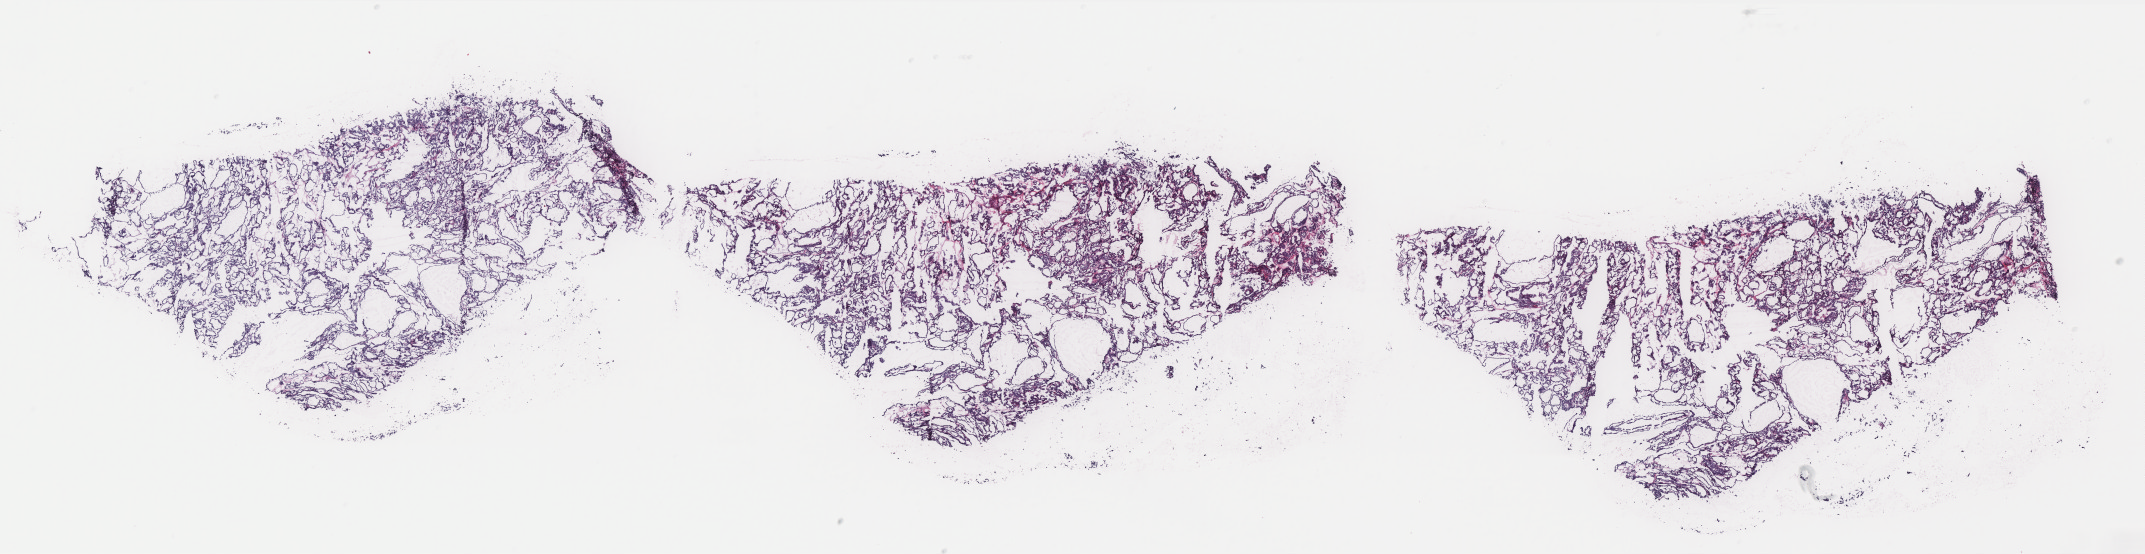
Whole-slide histology image, H&E, a low-resolution overview of the entire scanned area, about 34.4 x 8.9 mm (slide scanned at 40x). Frozen section from the top of the tissue portion. Sample: primary tumour, thyroid. Male patient; age at initial diagnosis 55 years. Pathologist review of this section (percent, as recorded): tumour cells 99%, tumour nuclei 95%, normal cells 0%, stromal cells 1%, necrosis 0%. Inflammatory infiltration, as recorded: lymphocyte infiltration 0%, monocyte infiltration 0%, neutrophil infiltration 0%.
• lymph nodes positive (case pathology): 0 of 5 examined
• AJCC pathologic stage: II (7th edition)
• diagnosis: Papillary adenocarcinoma, NOS (thyroid gland)